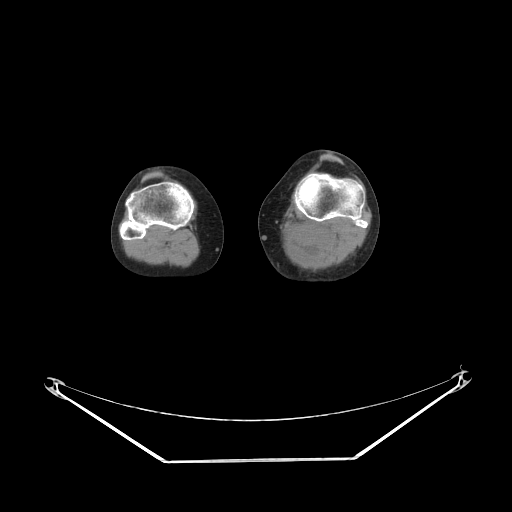
CT of an extremity soft-tissue mass (from a PET/CT study), one axial slice; position 161 of 223 along the scan axis; soft-tissue window (W 400 / L 40 HU); 3.75 mm slice thickness; 512 × 512 image matrix, field of view 500 × 500 mm. Female patient. Case-level facts recorded for this patient, not image findings: histological type: extraskeletal high grade osteogenic sarcoma; grade: high; site of the primary tumour: left calf.
Outlined on this slice (expert contour drawn on MRI and transferred to this co-registered scan by the dataset authors):
- gross tumour volume (mass): bounding box [x1, y1, x2, y2] px = [288, 231, 327, 259]